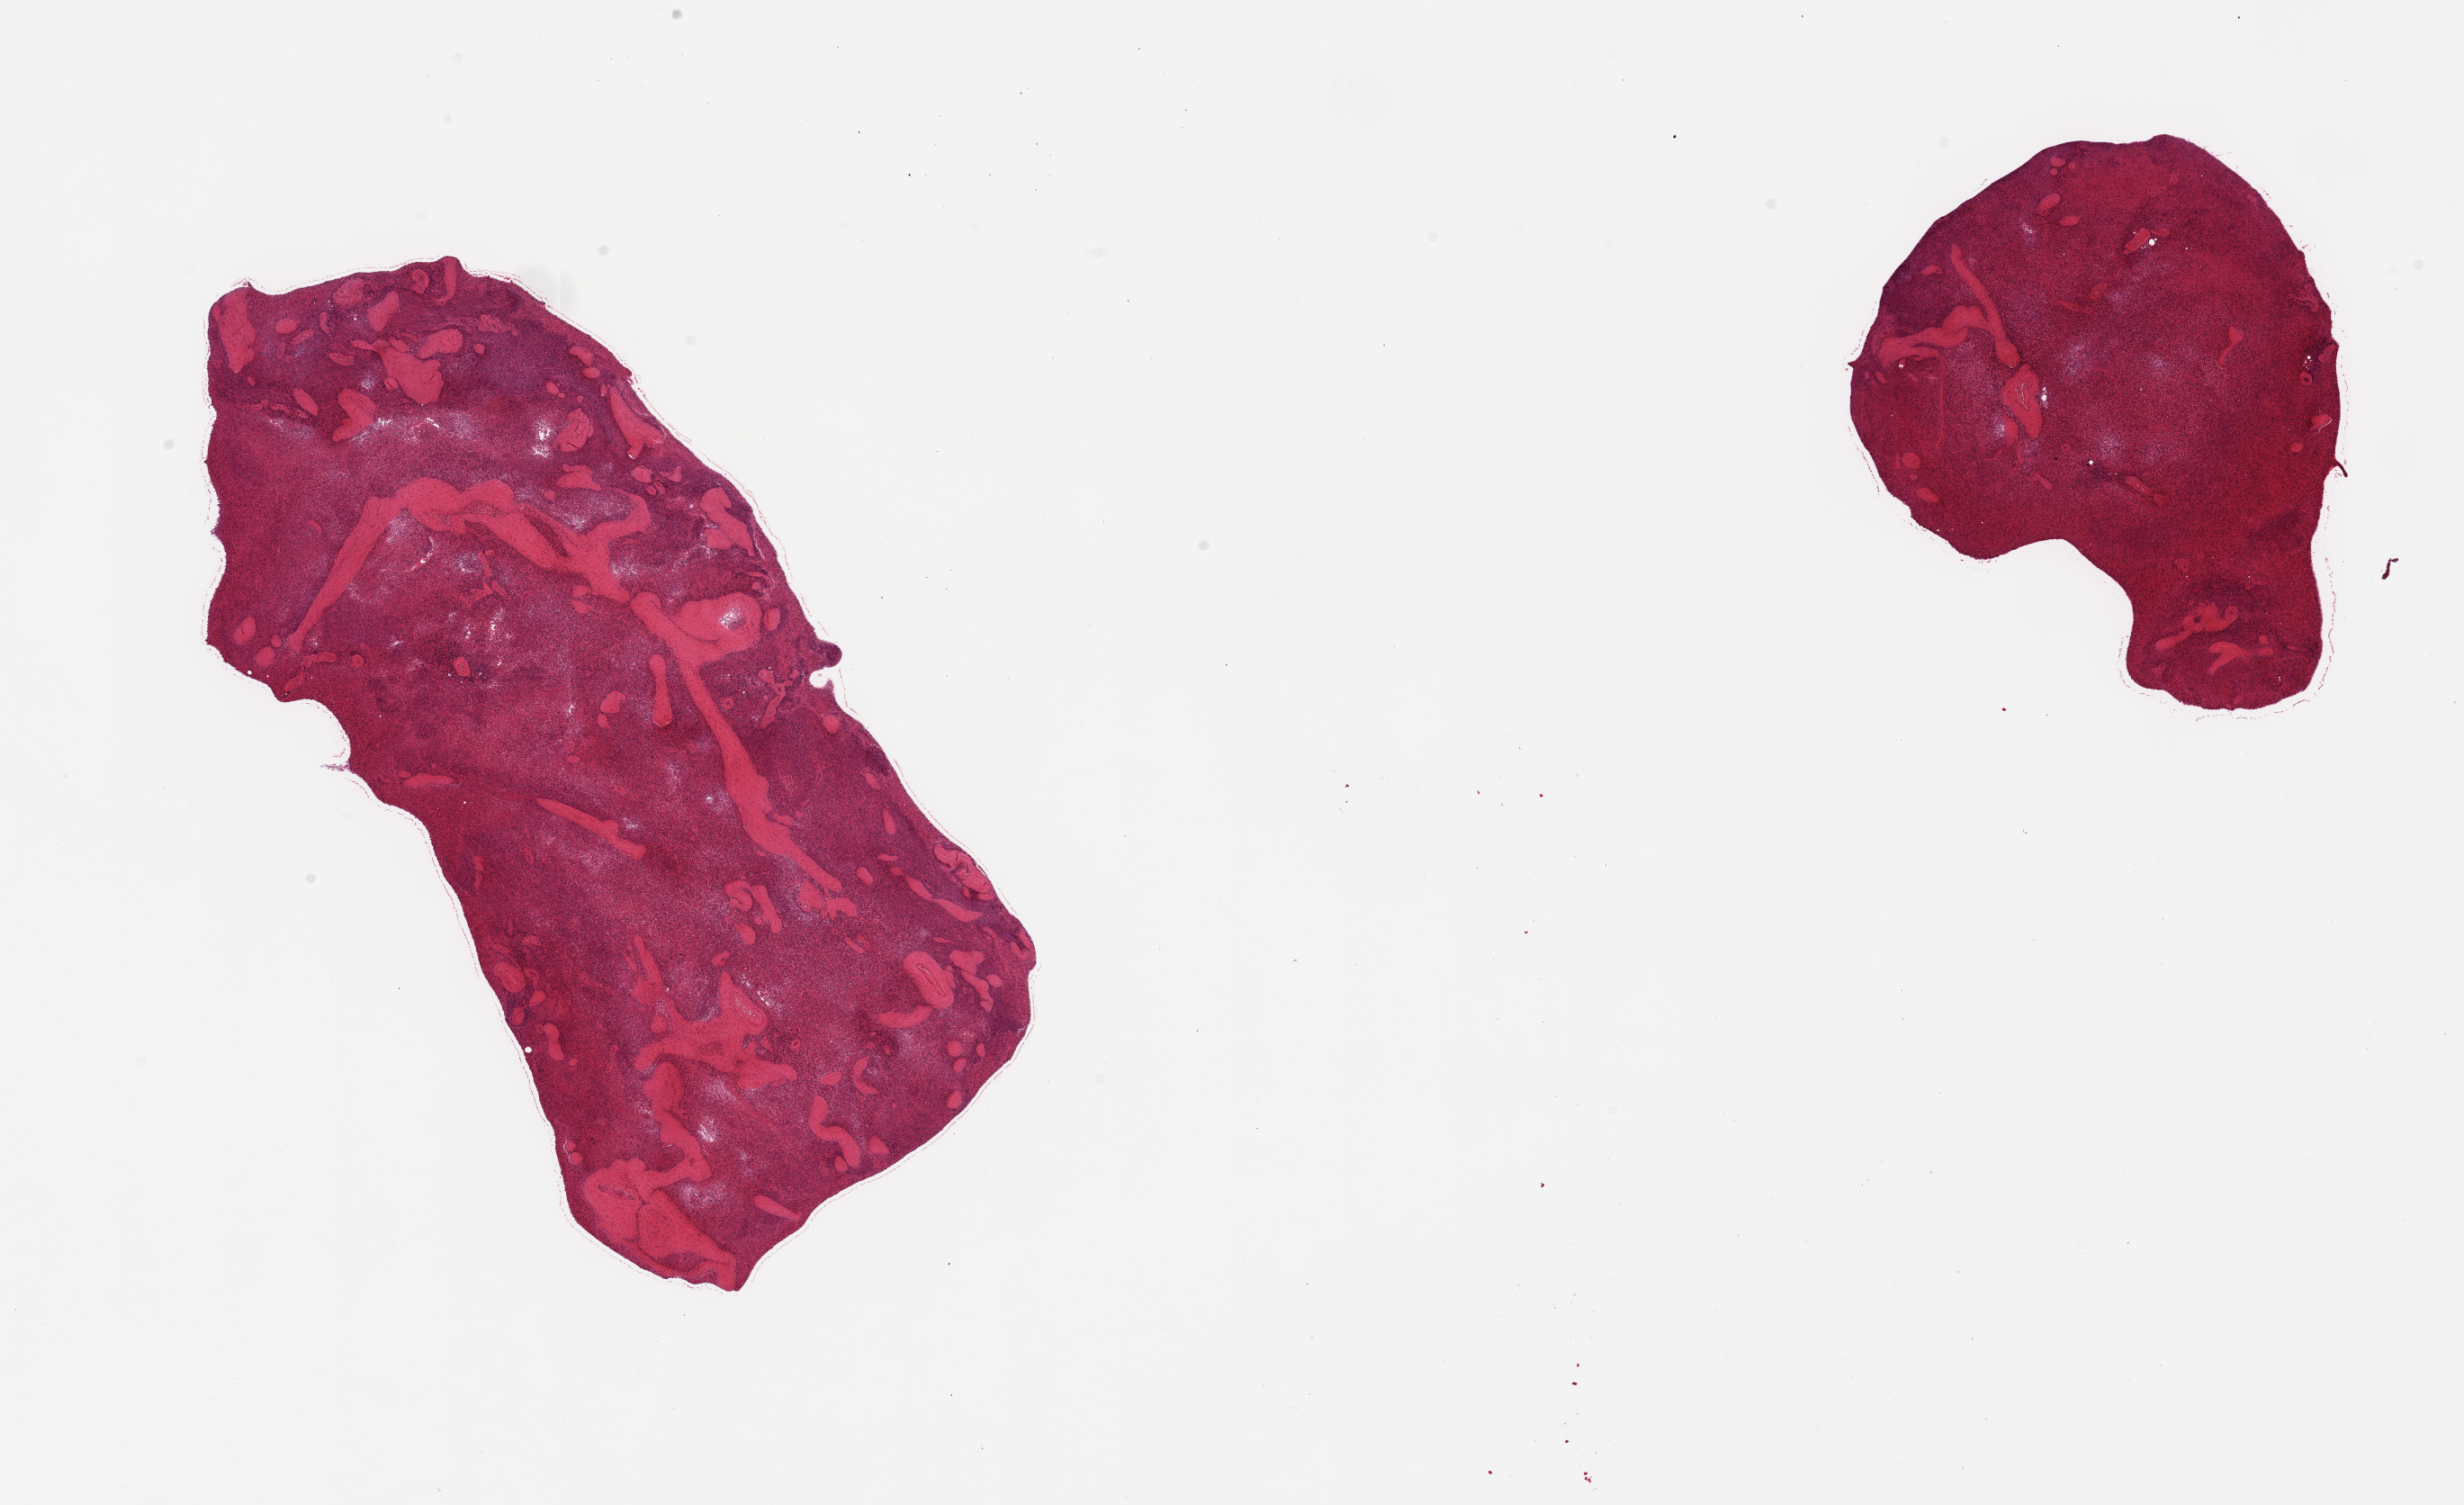
Digitized haematoxylin and eosin-stained section, brightfield, low-resolution overview of the scanned area, about 21.7 x 13.2 mm; PAXgene-fixed paraffin-embedded (PFPE) section; sampled site (target tissue): spleen; donor tissue sample. Donor: male.
Review note (as recorded): 2 pieces, marked congestion of red pulp.